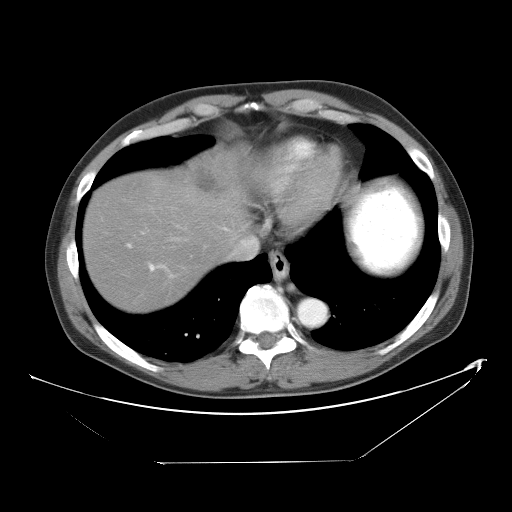
Contrast-enhanced abdominal CT, one axial slice. Position 46 of 53 along the scan axis. Reconstruction kernel STANDARD. 120 kVp. Intravenous contrast given. Soft-tissue window (W 400 / L 40 HU). 5 mm slice thickness. 512 × 512 image matrix, field of view 438 × 438 mm. Male patient, age 59 years. From the clinical record (not read from this slice): diagnosis: colorectal cancer liver metastases, imaged before liver resection; multiple liver metastases: yes; largest metastasis: 8.5 cm.
Annotated regions visible in this slice (expert manual segmentation):
- hepatic veins: bounding box [x1, y1, x2, y2] px = [234, 238, 258, 258]
- liver: [85, 155, 247, 311]
- planned liver remnant (the part of the liver to remain after resection): [85, 177, 225, 311]
- portal vein (with intrahepatic branches): [142, 232, 155, 271]
- liver metastasis: [192, 162, 227, 195]